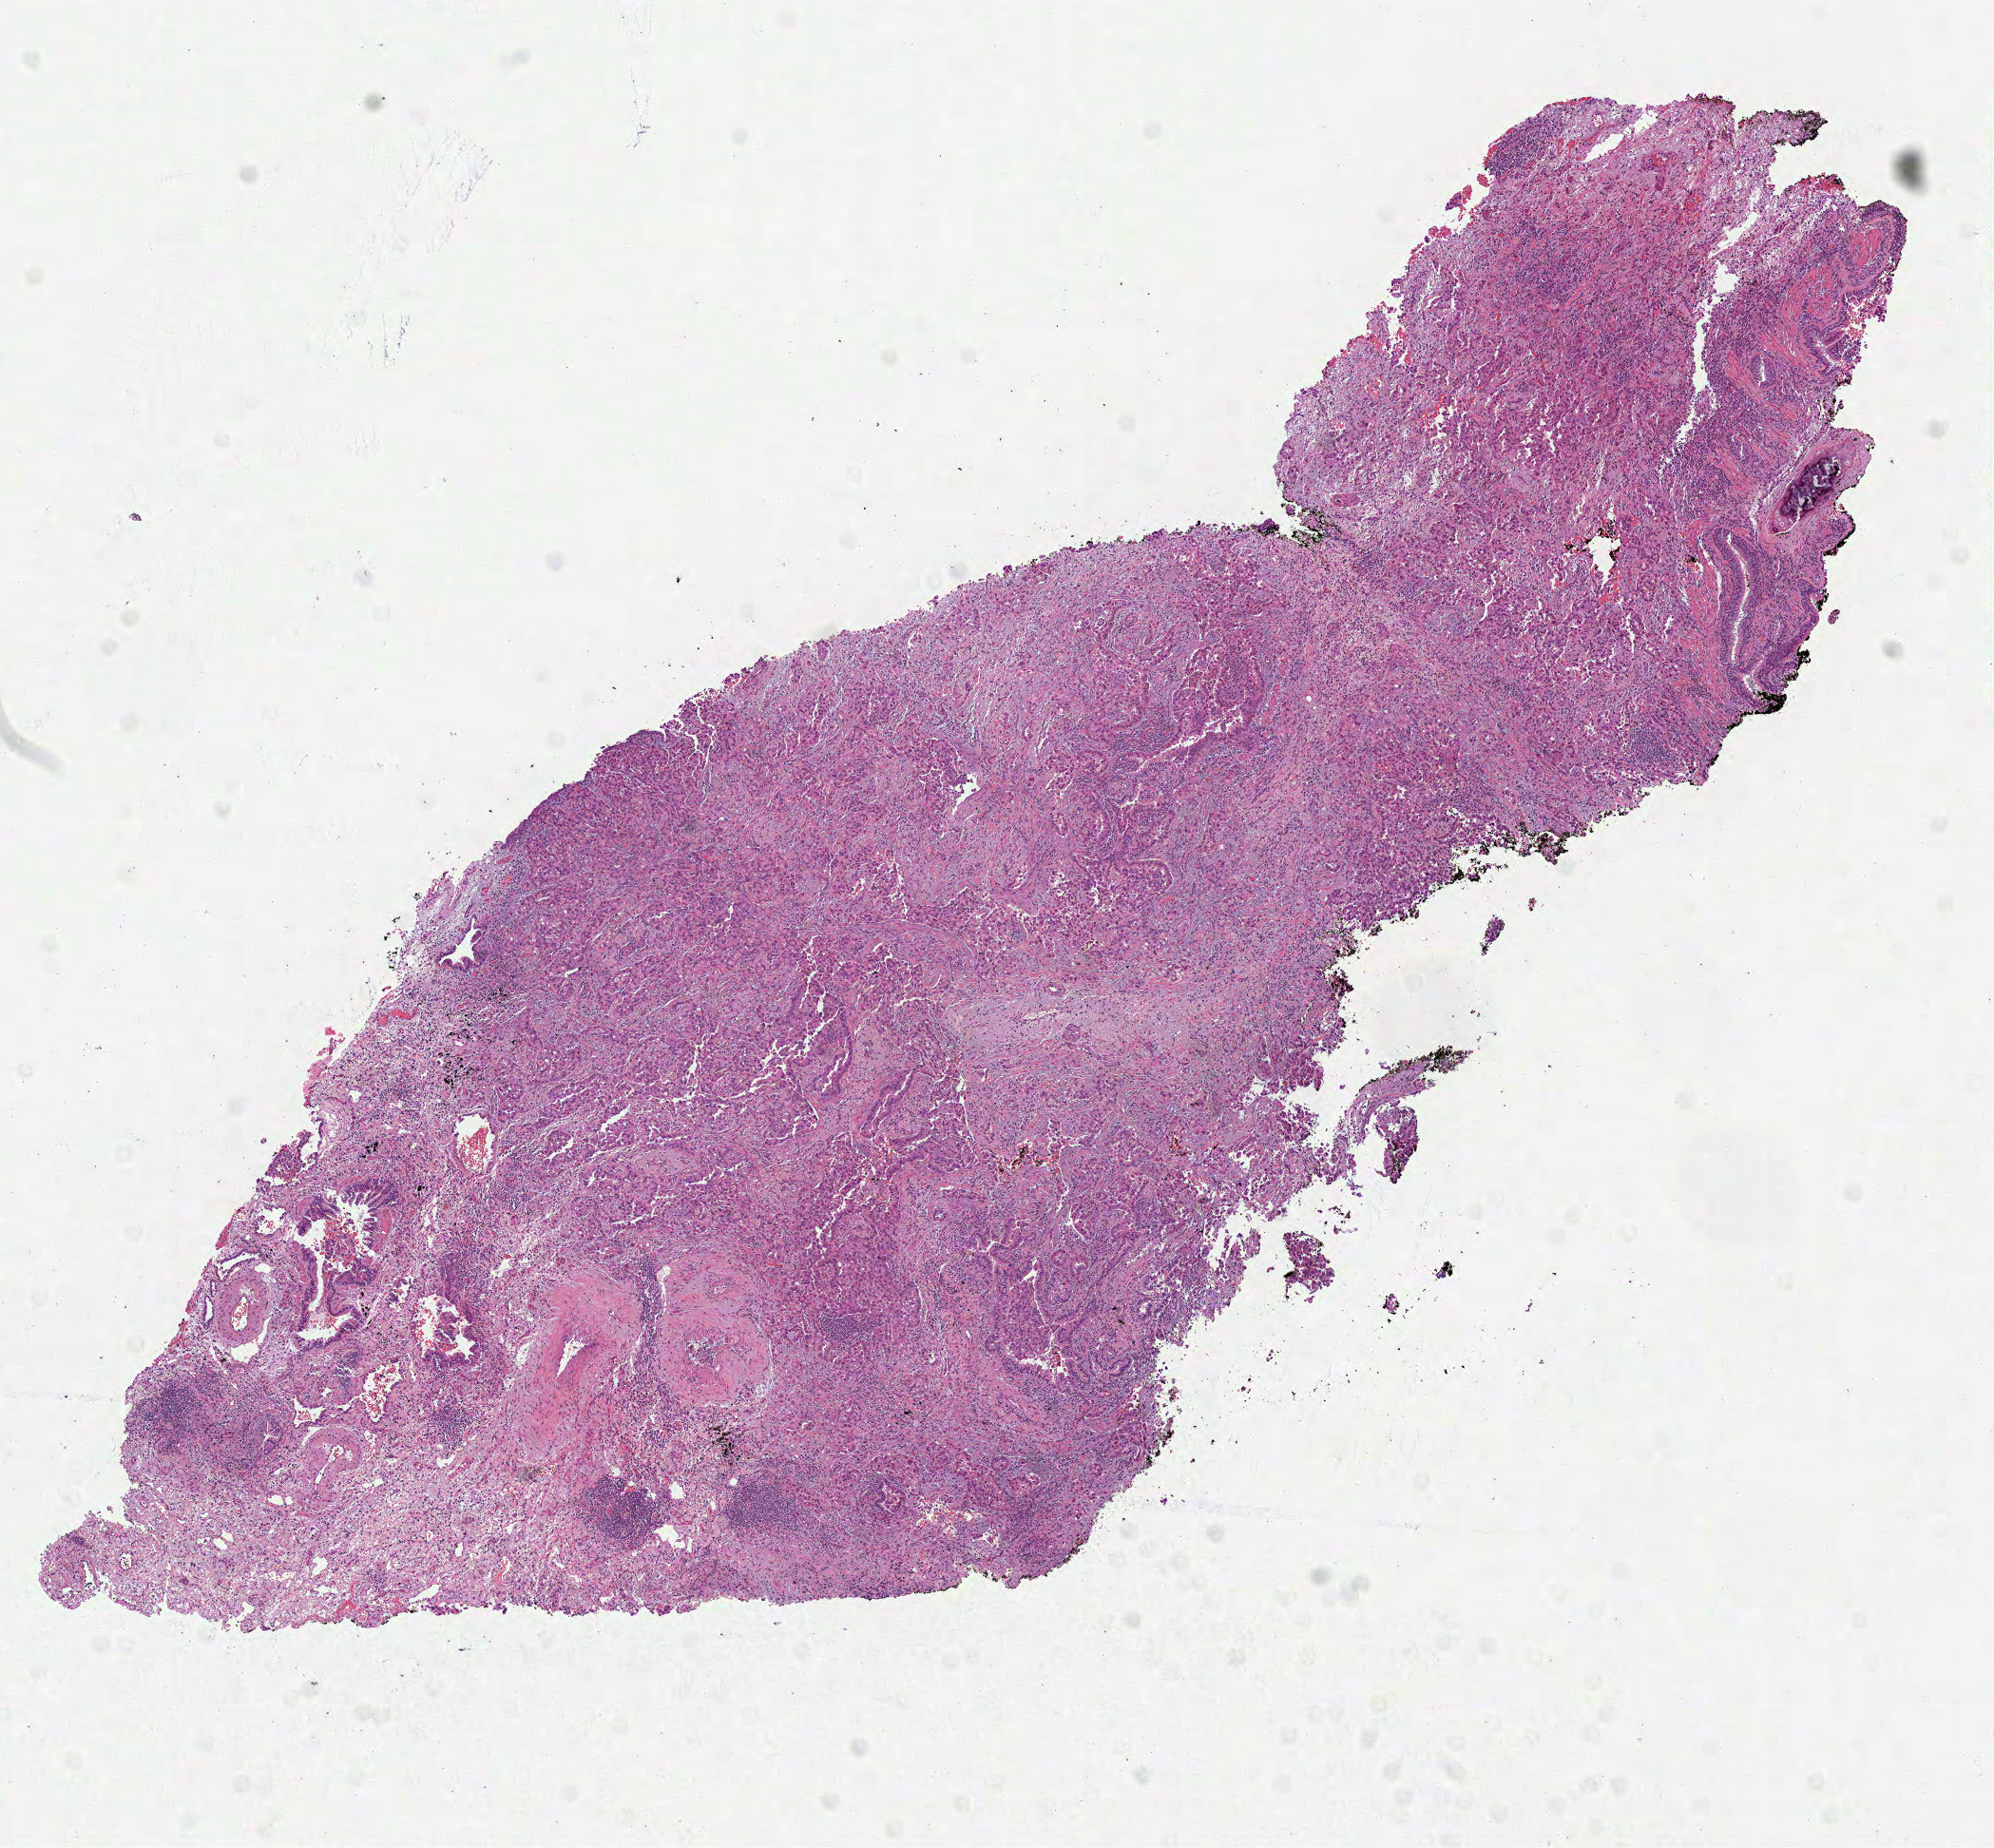
Digitized H&E-stained tissue section (whole slide), a low-resolution overview of the entire scanned area, about 8.5 x 7.8 mm; formalin-fixed paraffin-embedded (FFPE) diagnostic section; primary tumour sample from the lung. Female, age 72 years at initial diagnosis.
- TNM: T1b N0 MX
- AJCC pathologic stage: IA
- pathologic diagnosis: Adenocarcinoma, NOS